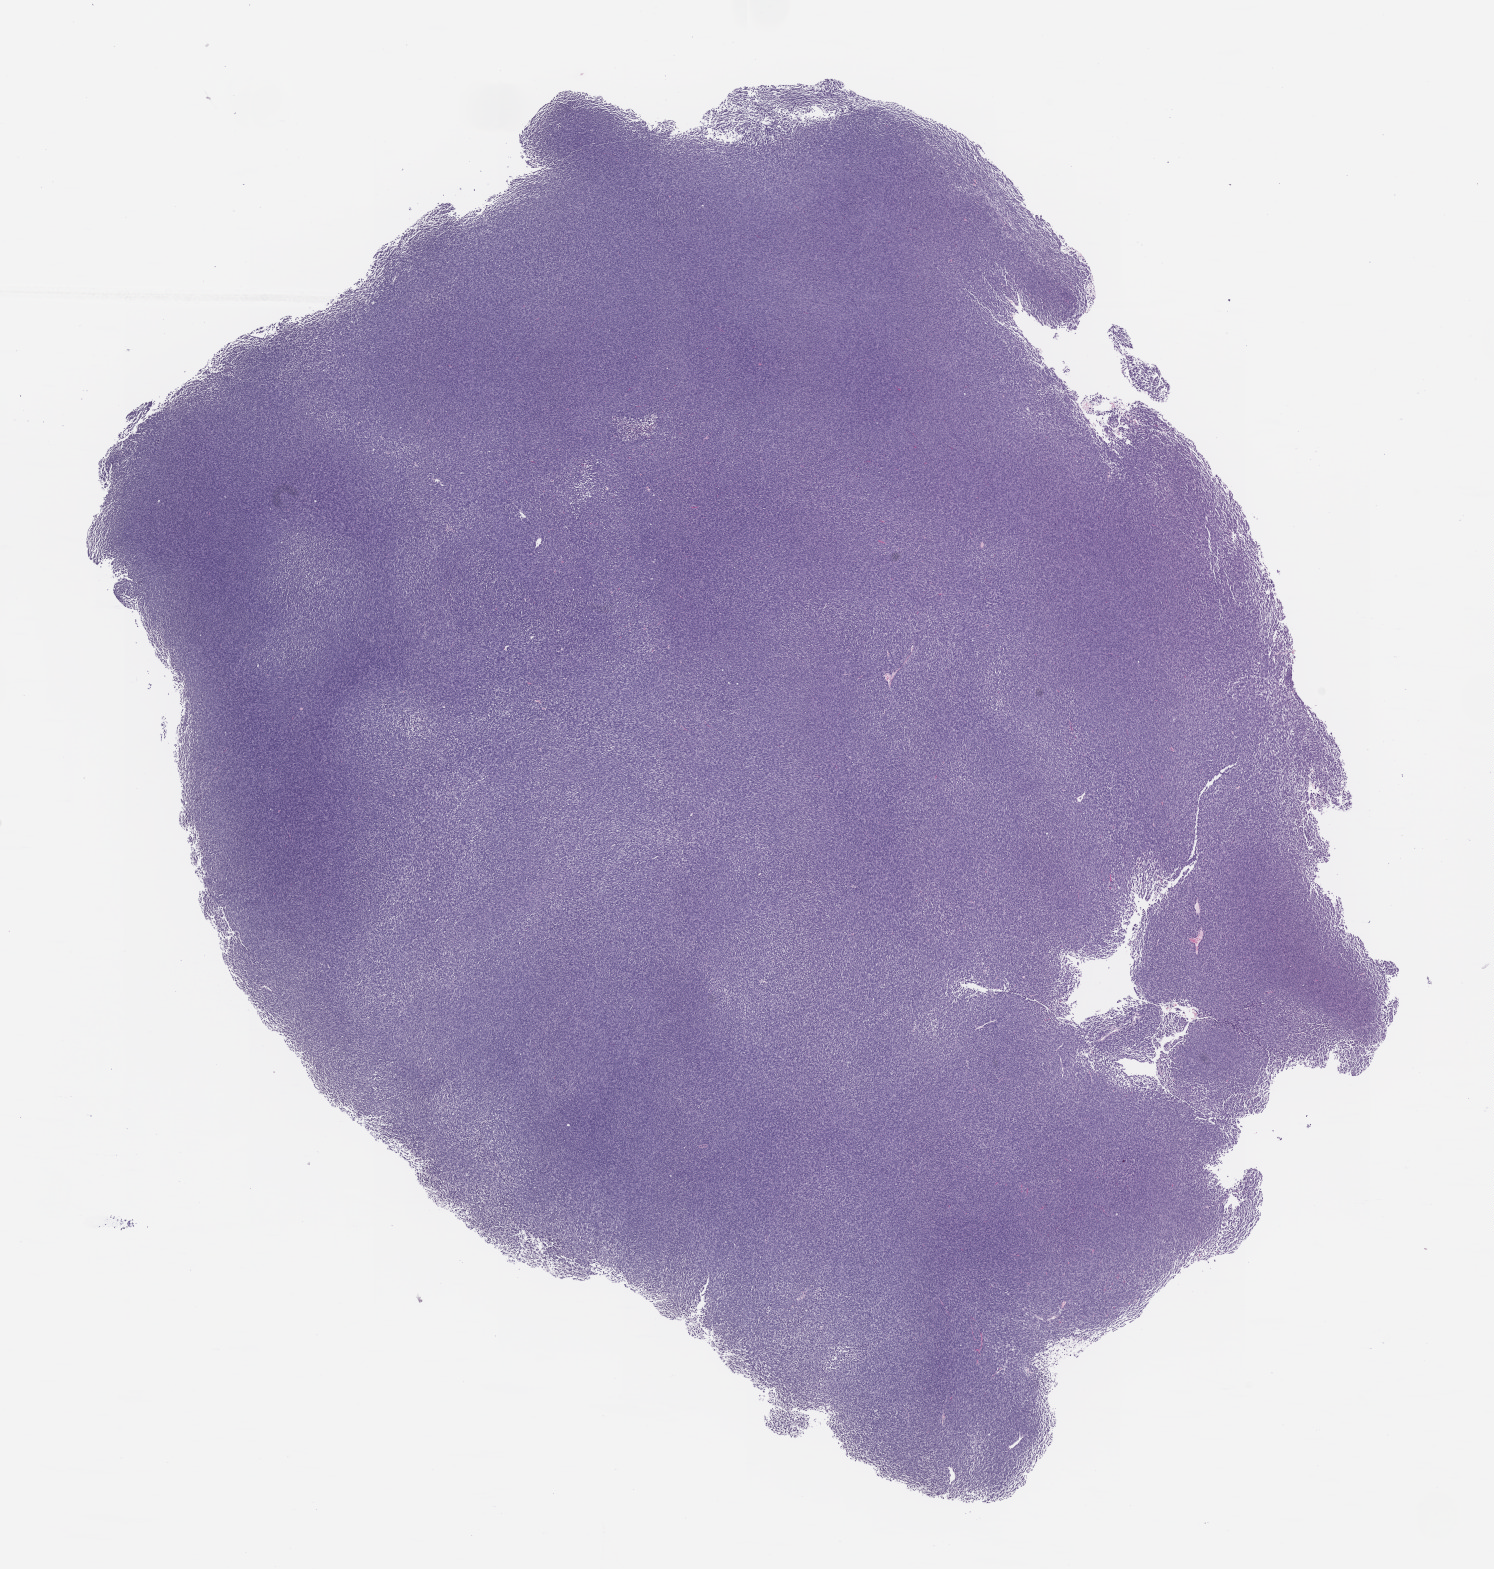
Whole-slide image, H&E: patient-derived xenograft (human tumor grown in a mouse), passage 2, whole scanned area (about 12.0 x 12.6 mm) shown as a low-resolution overview, FFPE section, originating tumor site category: musculoskeletal.
Originating patient diagnosis: Synovial Sarcoma.